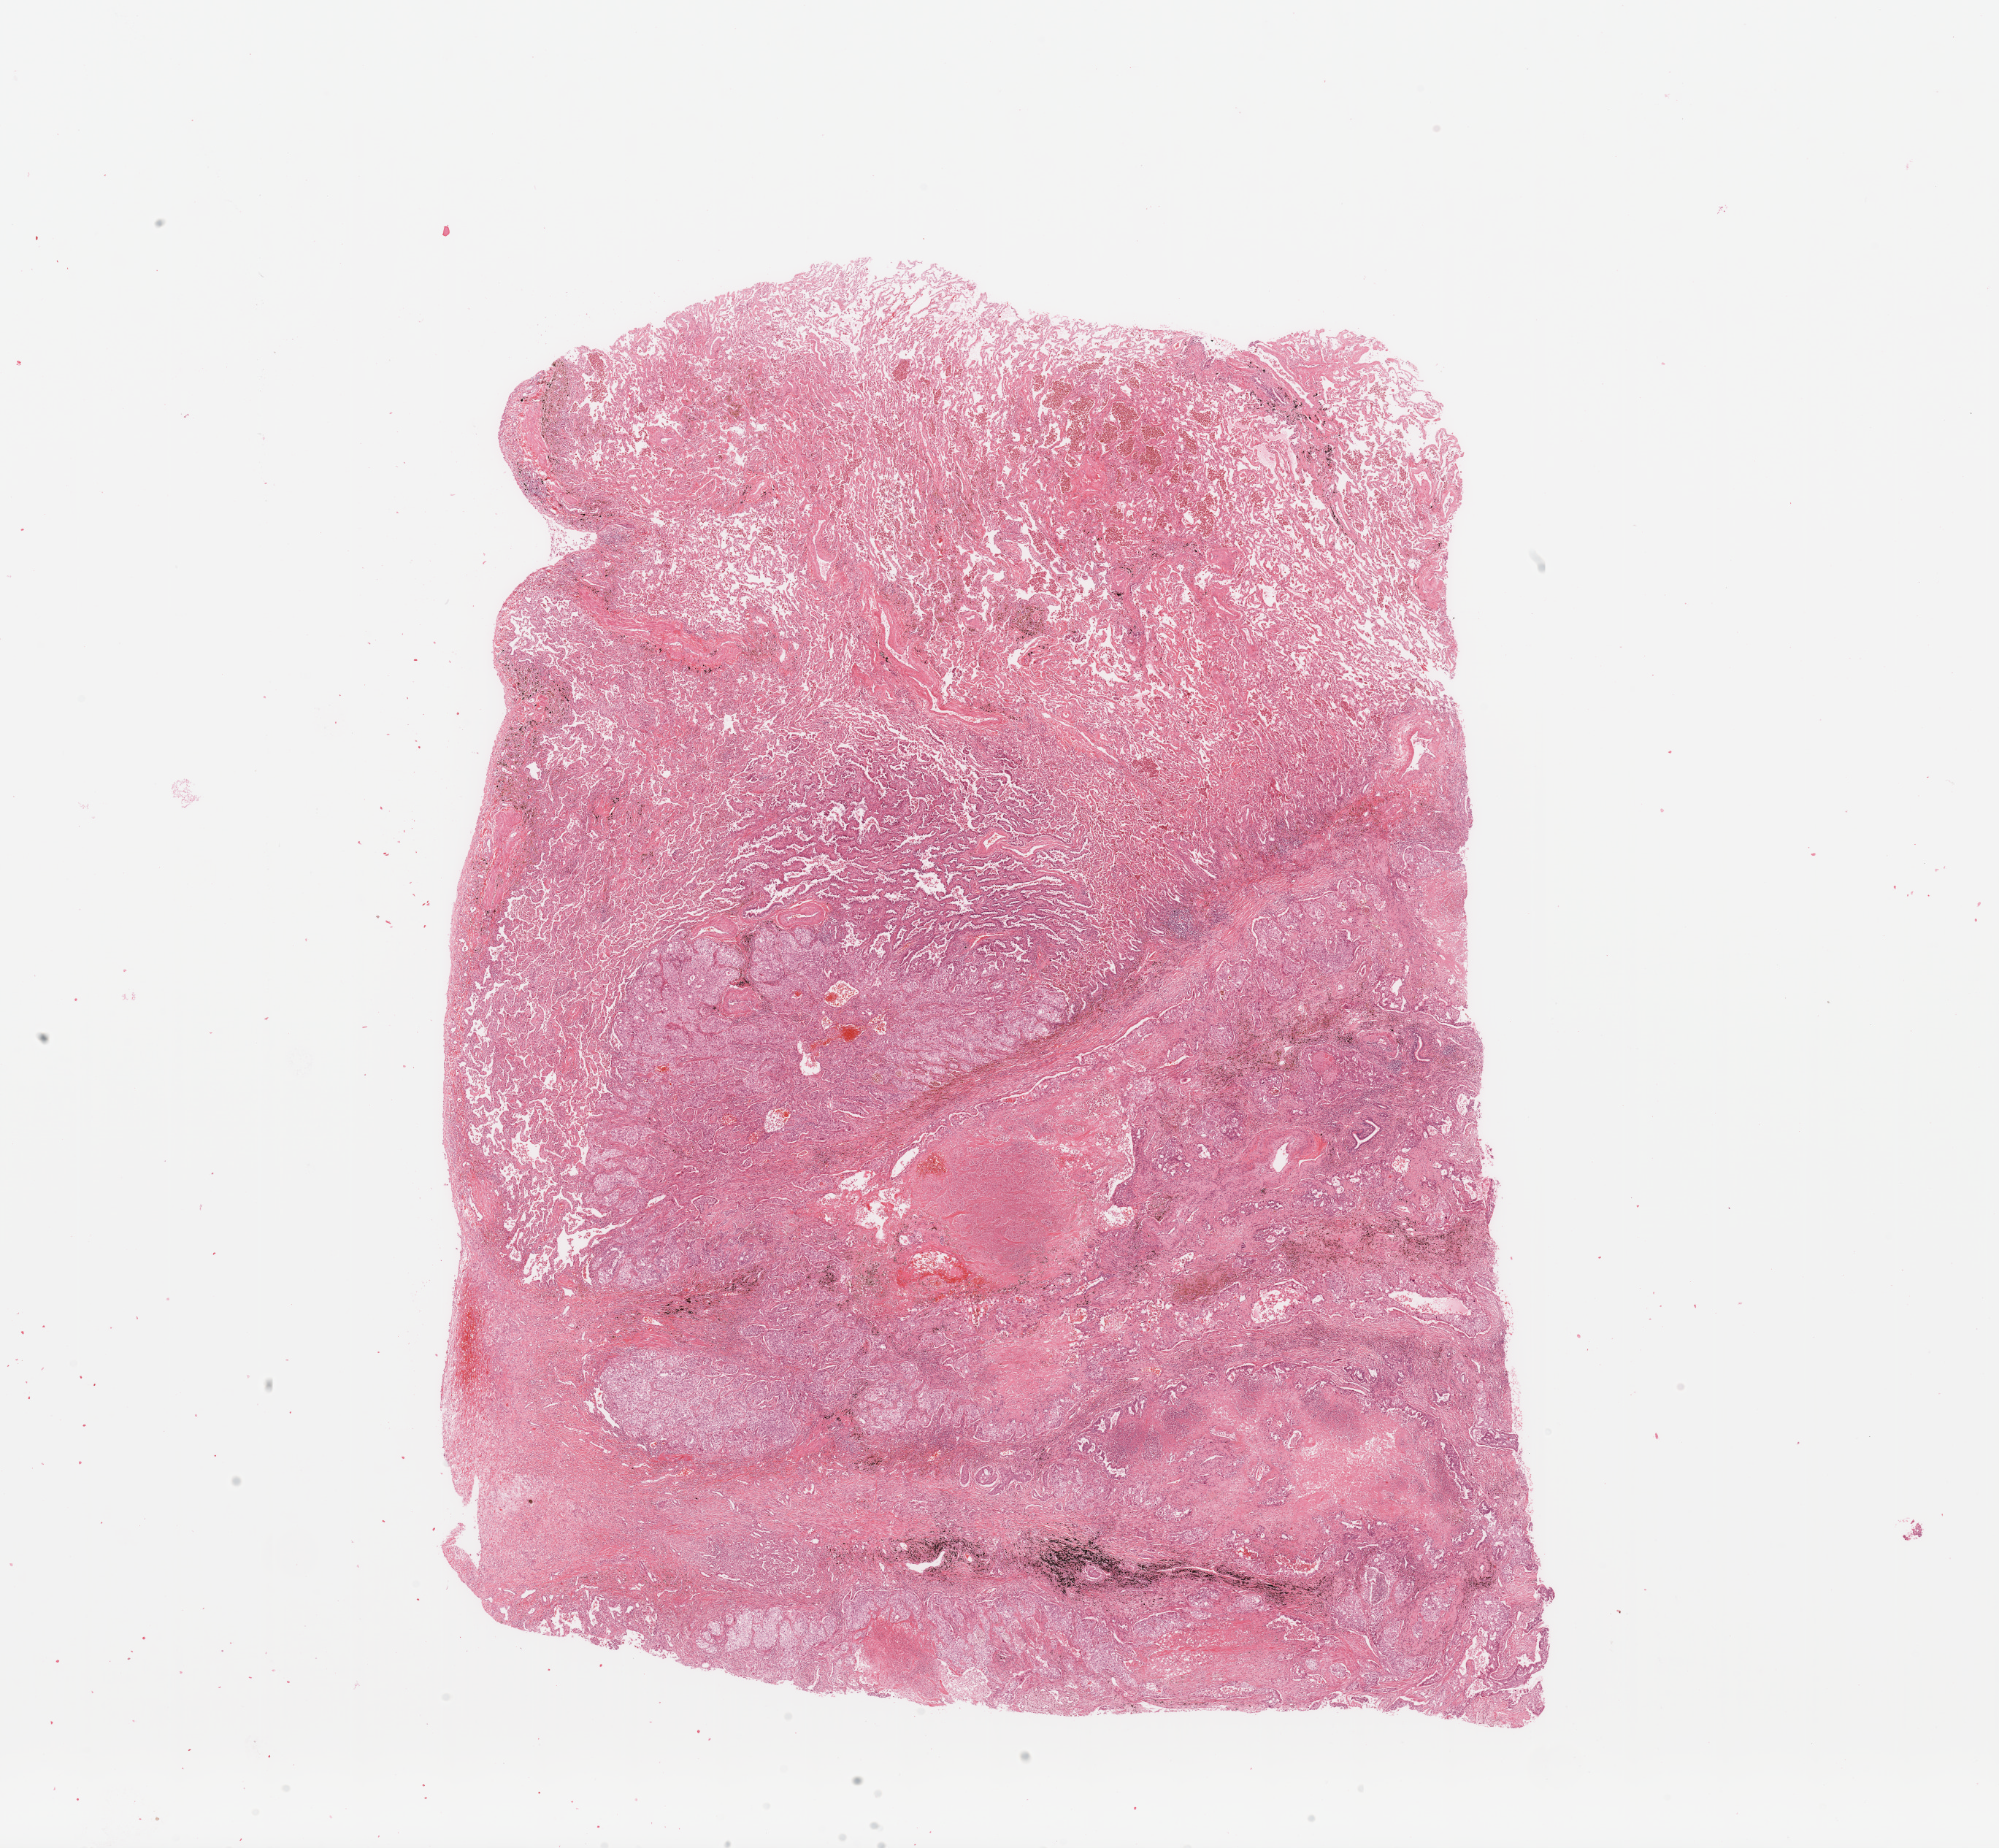
H&E-stained whole-slide image — a low-resolution overview of the entire scanned area, about 21.7 x 20.0 mm (slide scanned at 20x), lung, tumour tissue. 57-year-old male patient. Histologic grade: G2 (moderately differentiated).
• diagnosis: Adenocarcinoma, NOS
• AJCC pathologic stage: IB